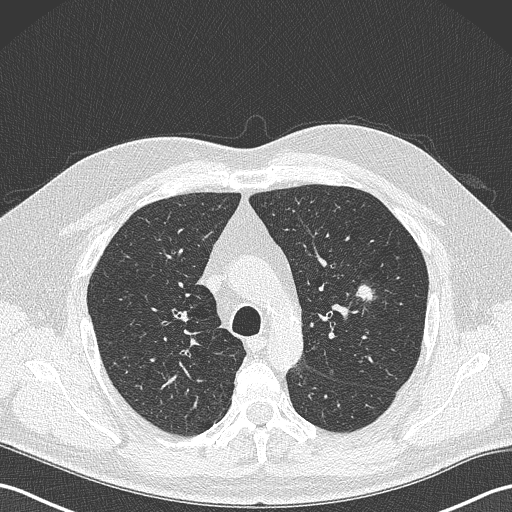
Low-dose screening chest CT, one axial slice. Position 243 of 343 along the scan axis. Reconstruction kernel B50f. 120 kVp. Lung window (W 1500 / L -600 HU). 512 × 512 image matrix, field of view 350 × 350 mm.
Annotated regions visible in this slice (manually delineated by an expert):
- lesion 1 (tumor, upper lobe of left lung): box from (x=356, y=284) to (x=377, y=303) px